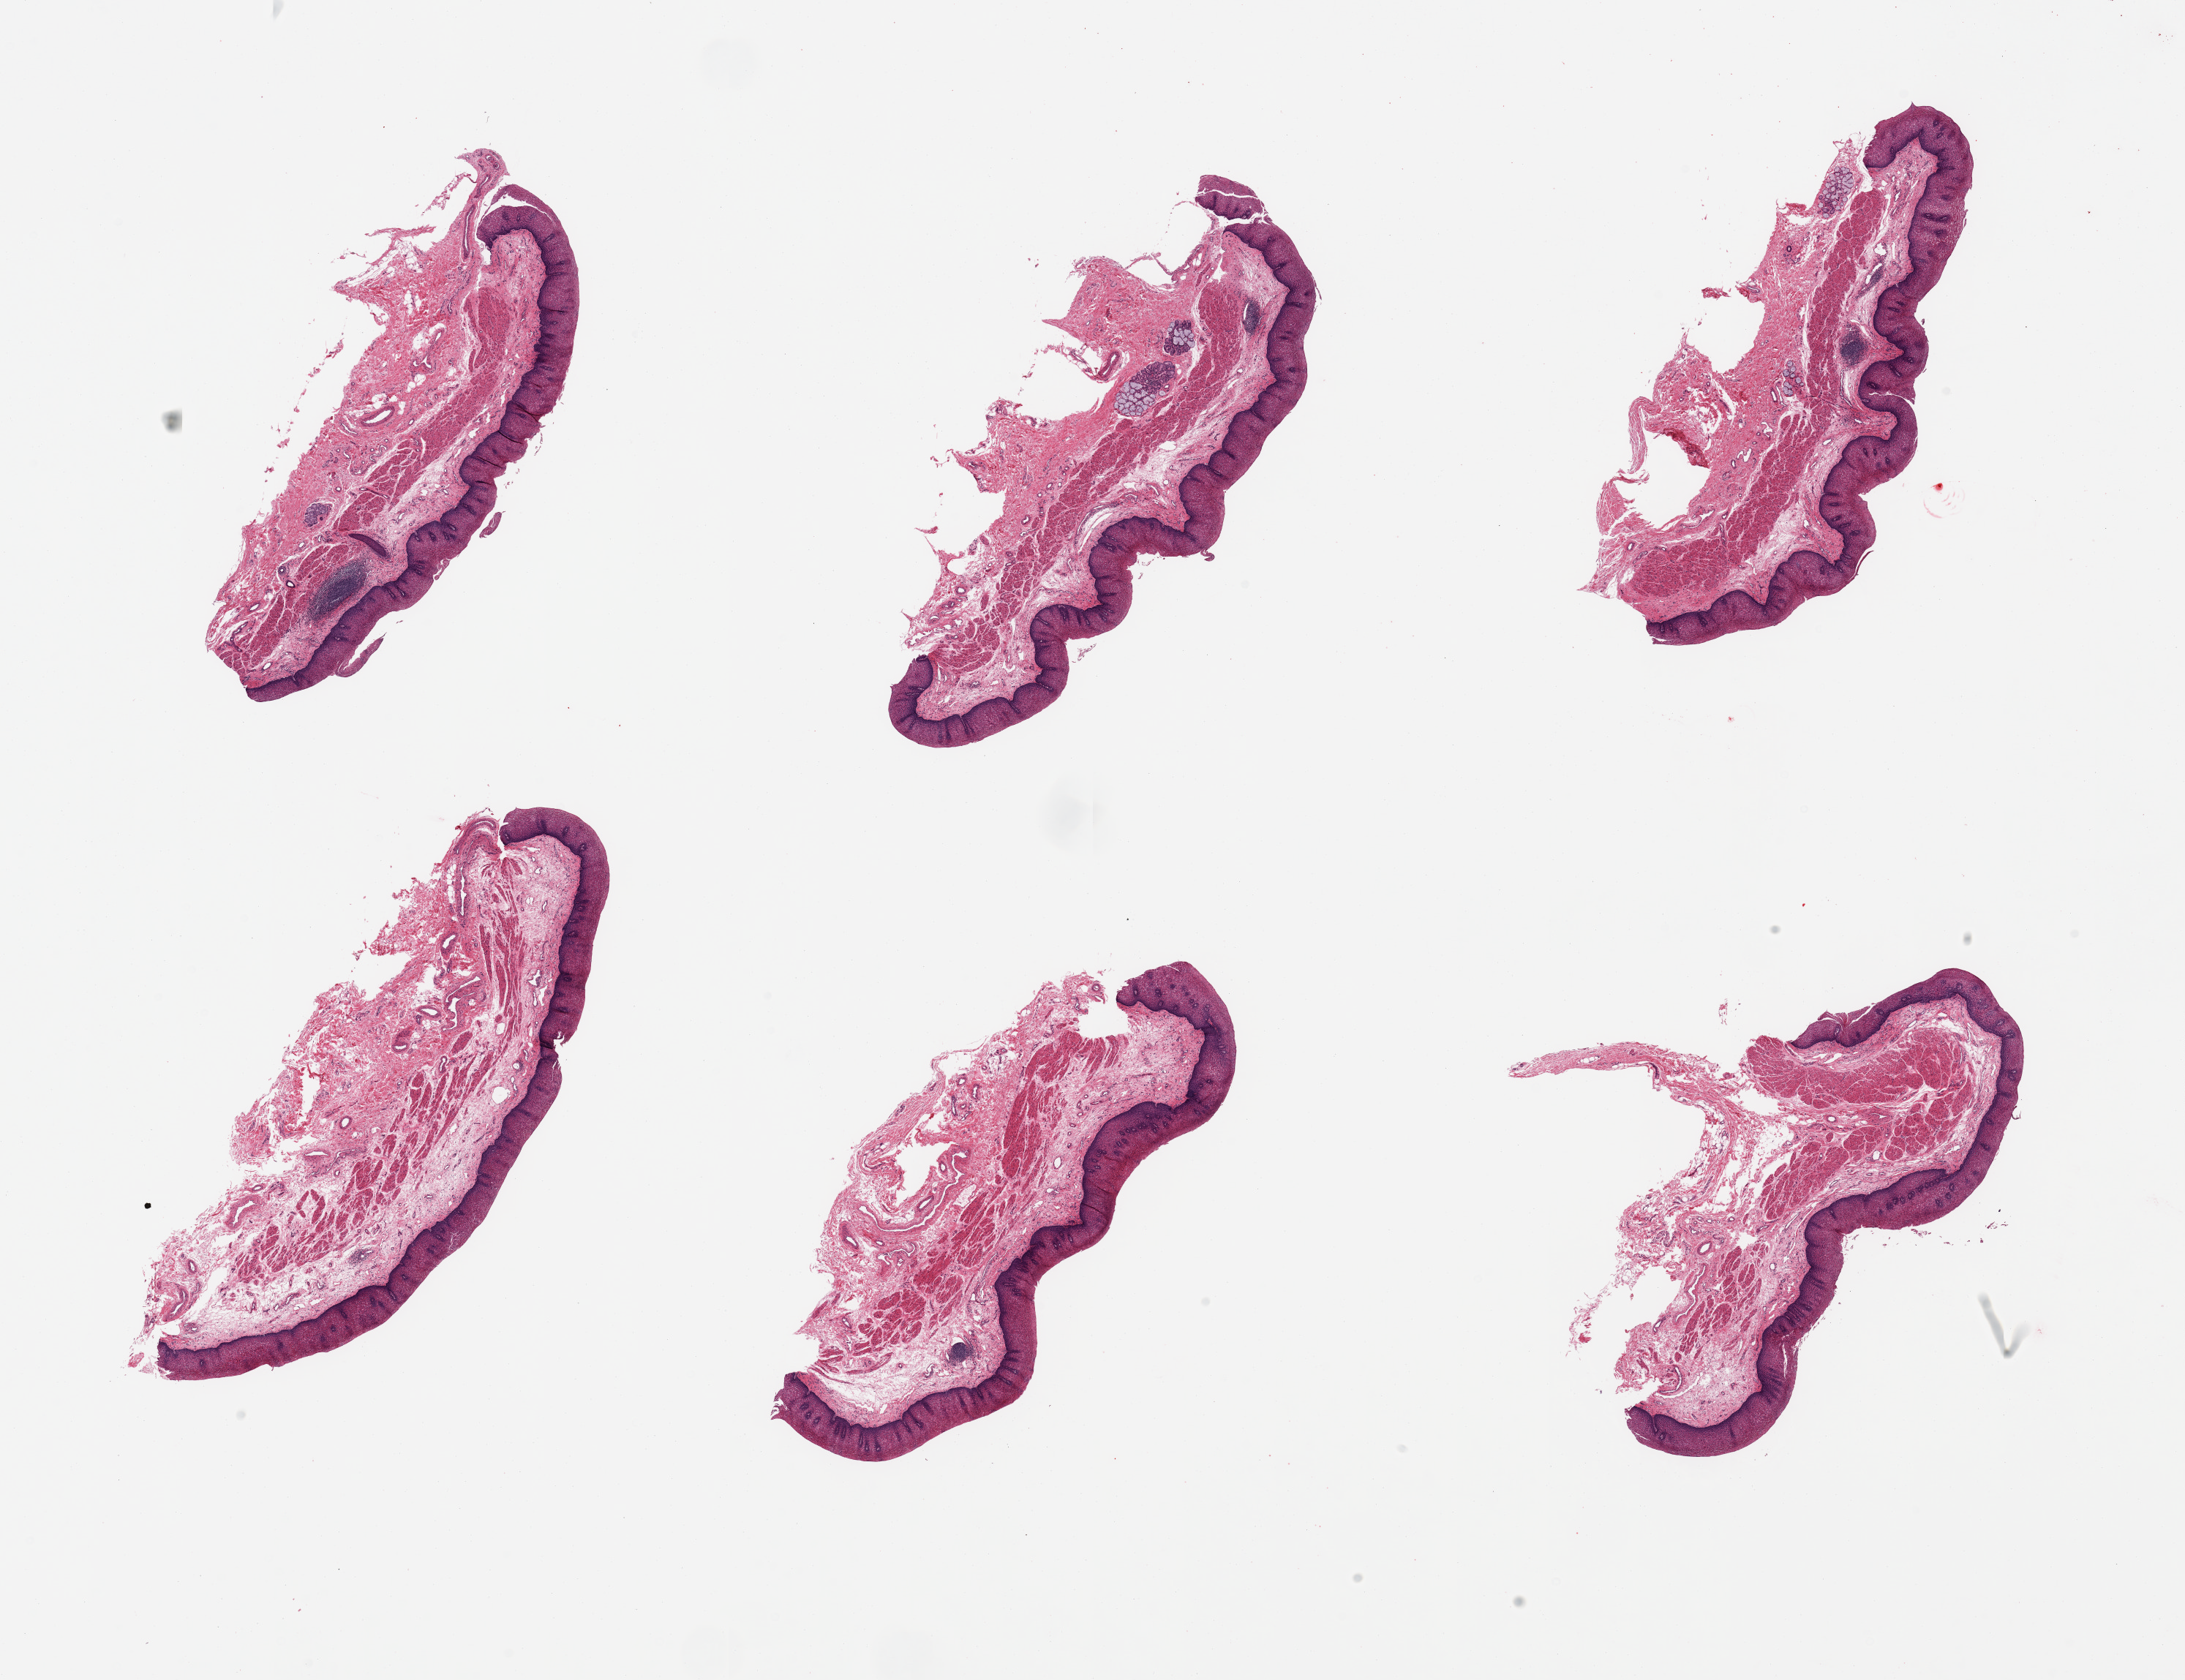
Digitized haematoxylin and eosin-stained section, brightfield, whole scanned area (about 23.6 x 18.2 mm, slide scanned at 20x) shown as a low-resolution overview. PAXgene-fixed, paraffin-embedded tissue. Section of esophageal mucous membrane (target tissue). Tissue donor sample.
Pathologist's review note for this sample: 6 pieces; includes few clusters of submucosal glands and lymphoid aggregates.